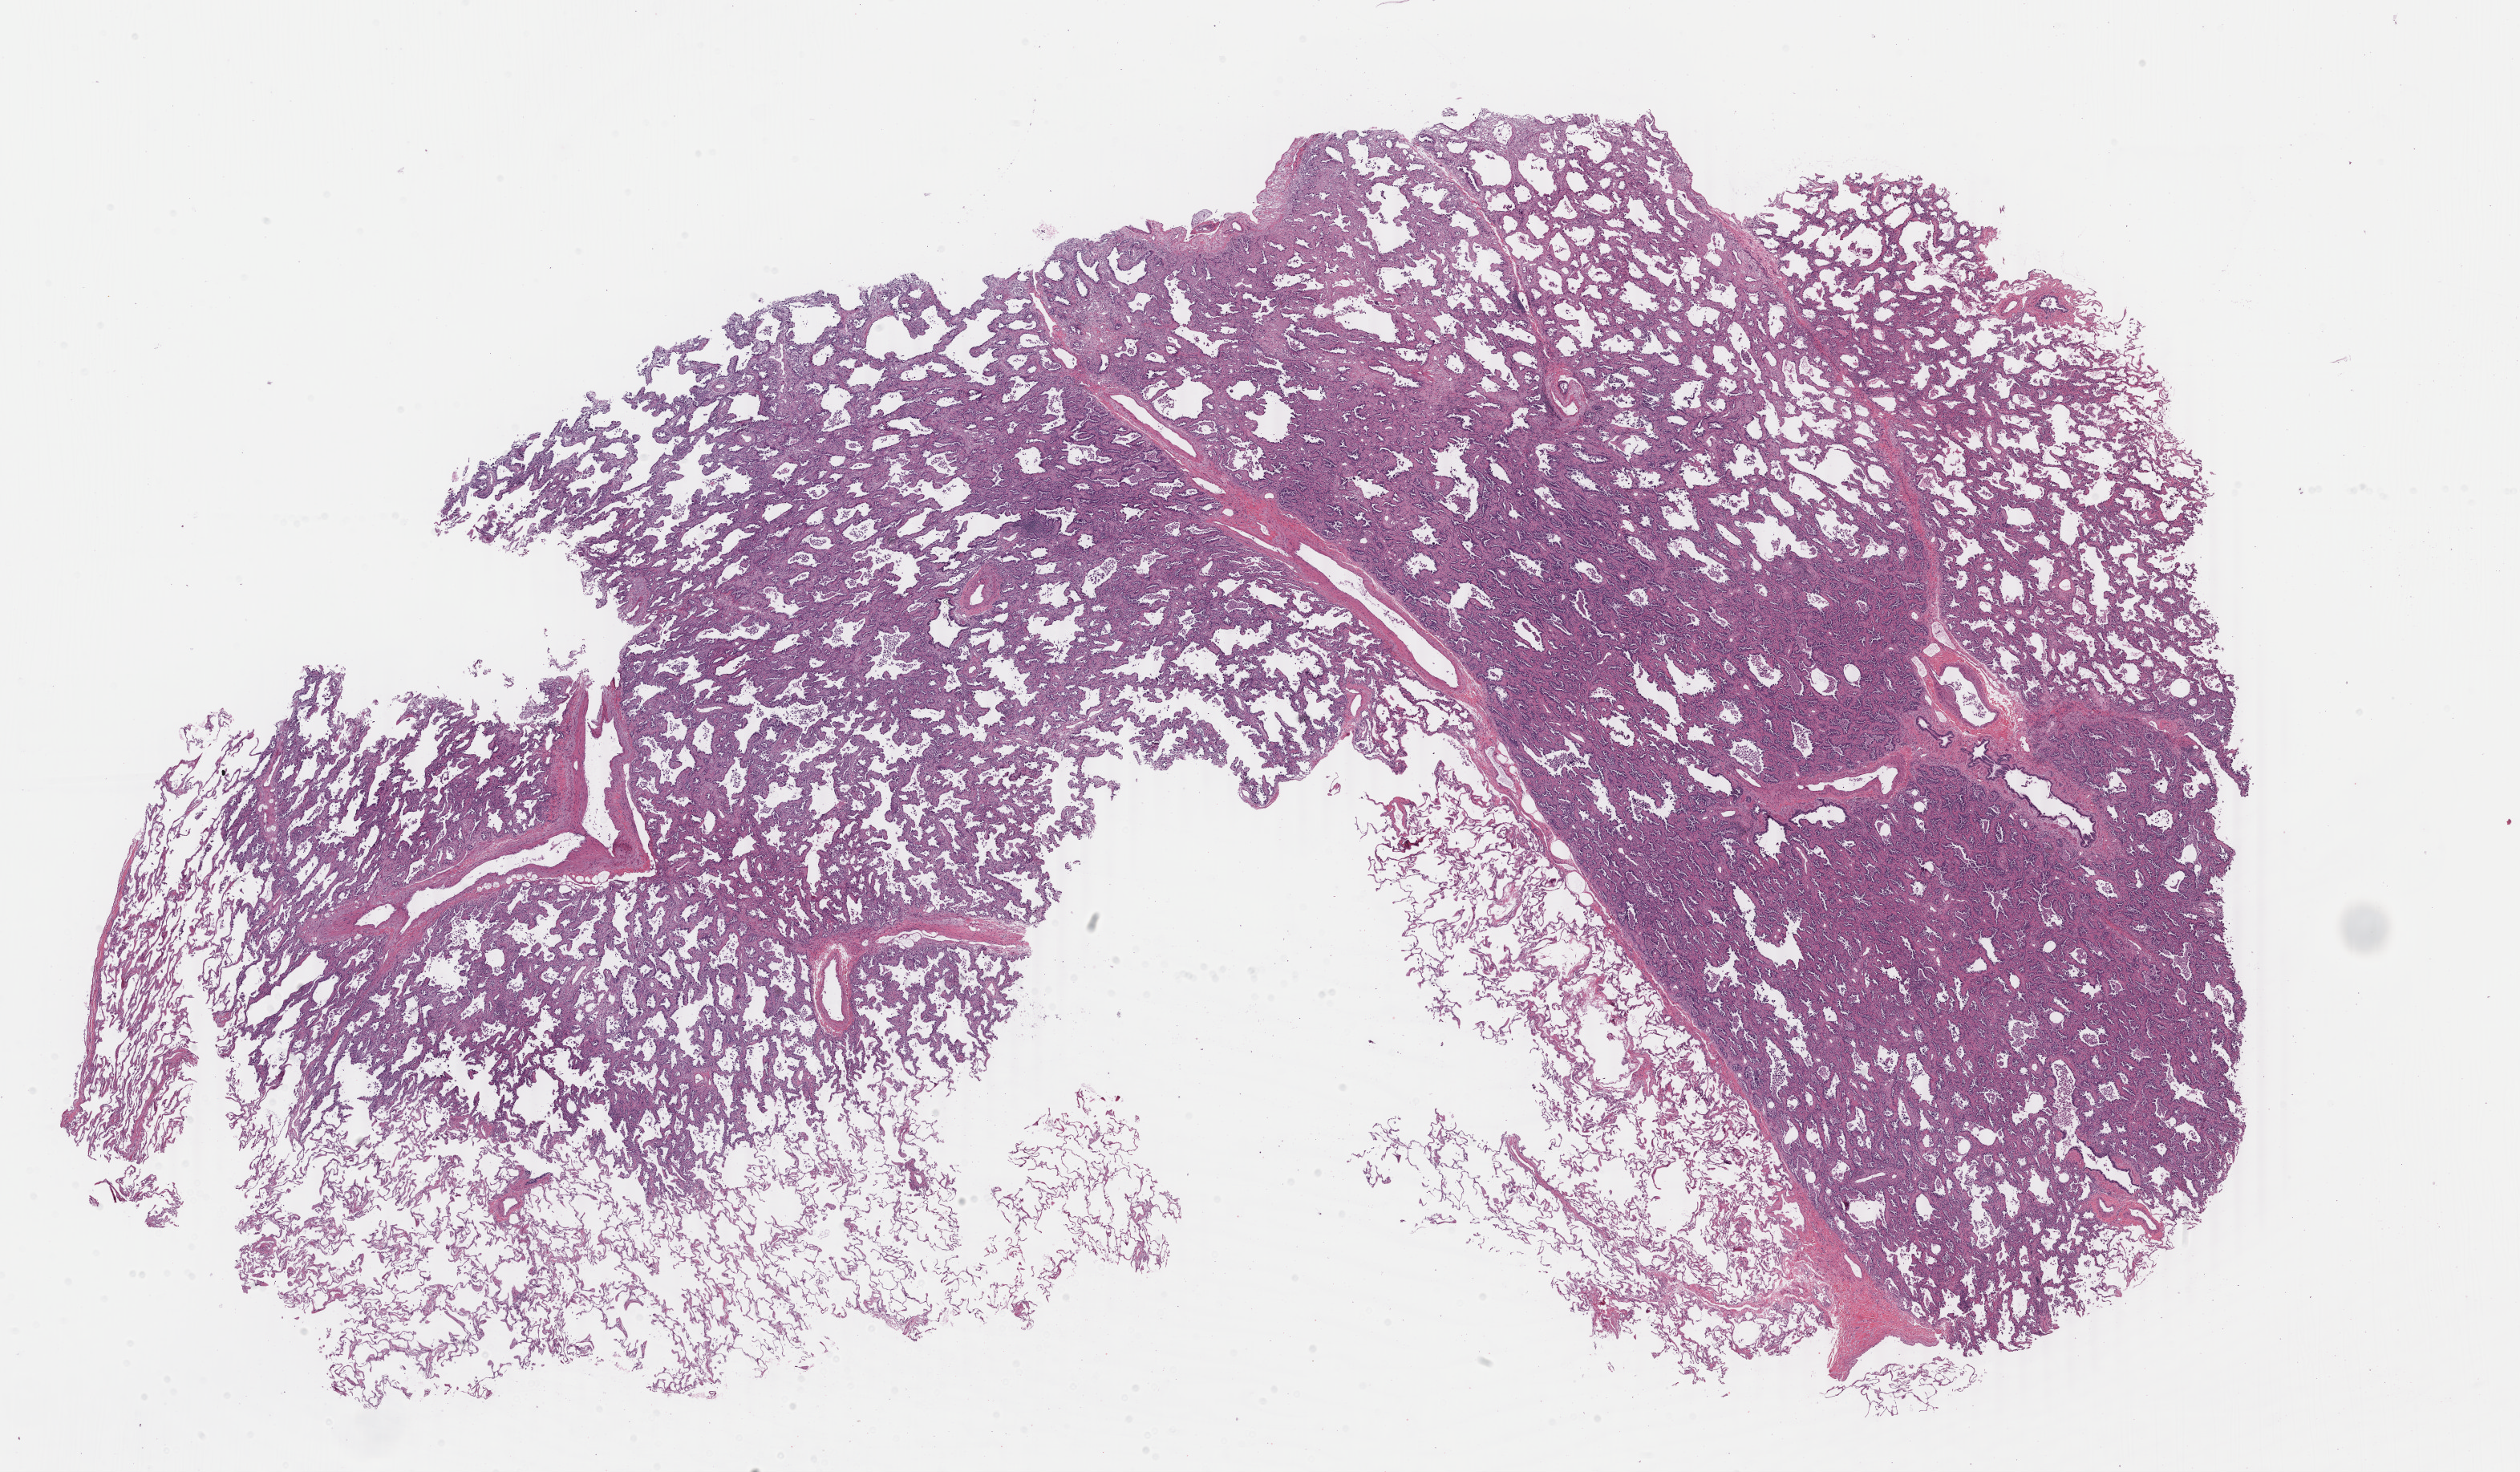
Whole-slide histology image, H&E — whole scanned area (about 25.0 x 14.6 mm, from a 40x scan) shown as a low-resolution overview; formalin-fixed paraffin-embedded (FFPE) diagnostic section; primary tumour sample from the lung. Female, age 52 years at initial diagnosis.
Histologic diagnosis: Adenocarcinoma with mixed subtypes (upper lobe, lung). Laterality: right. AJCC pathologic stage: IA (7th edition). TNM: T1a N0 M0.